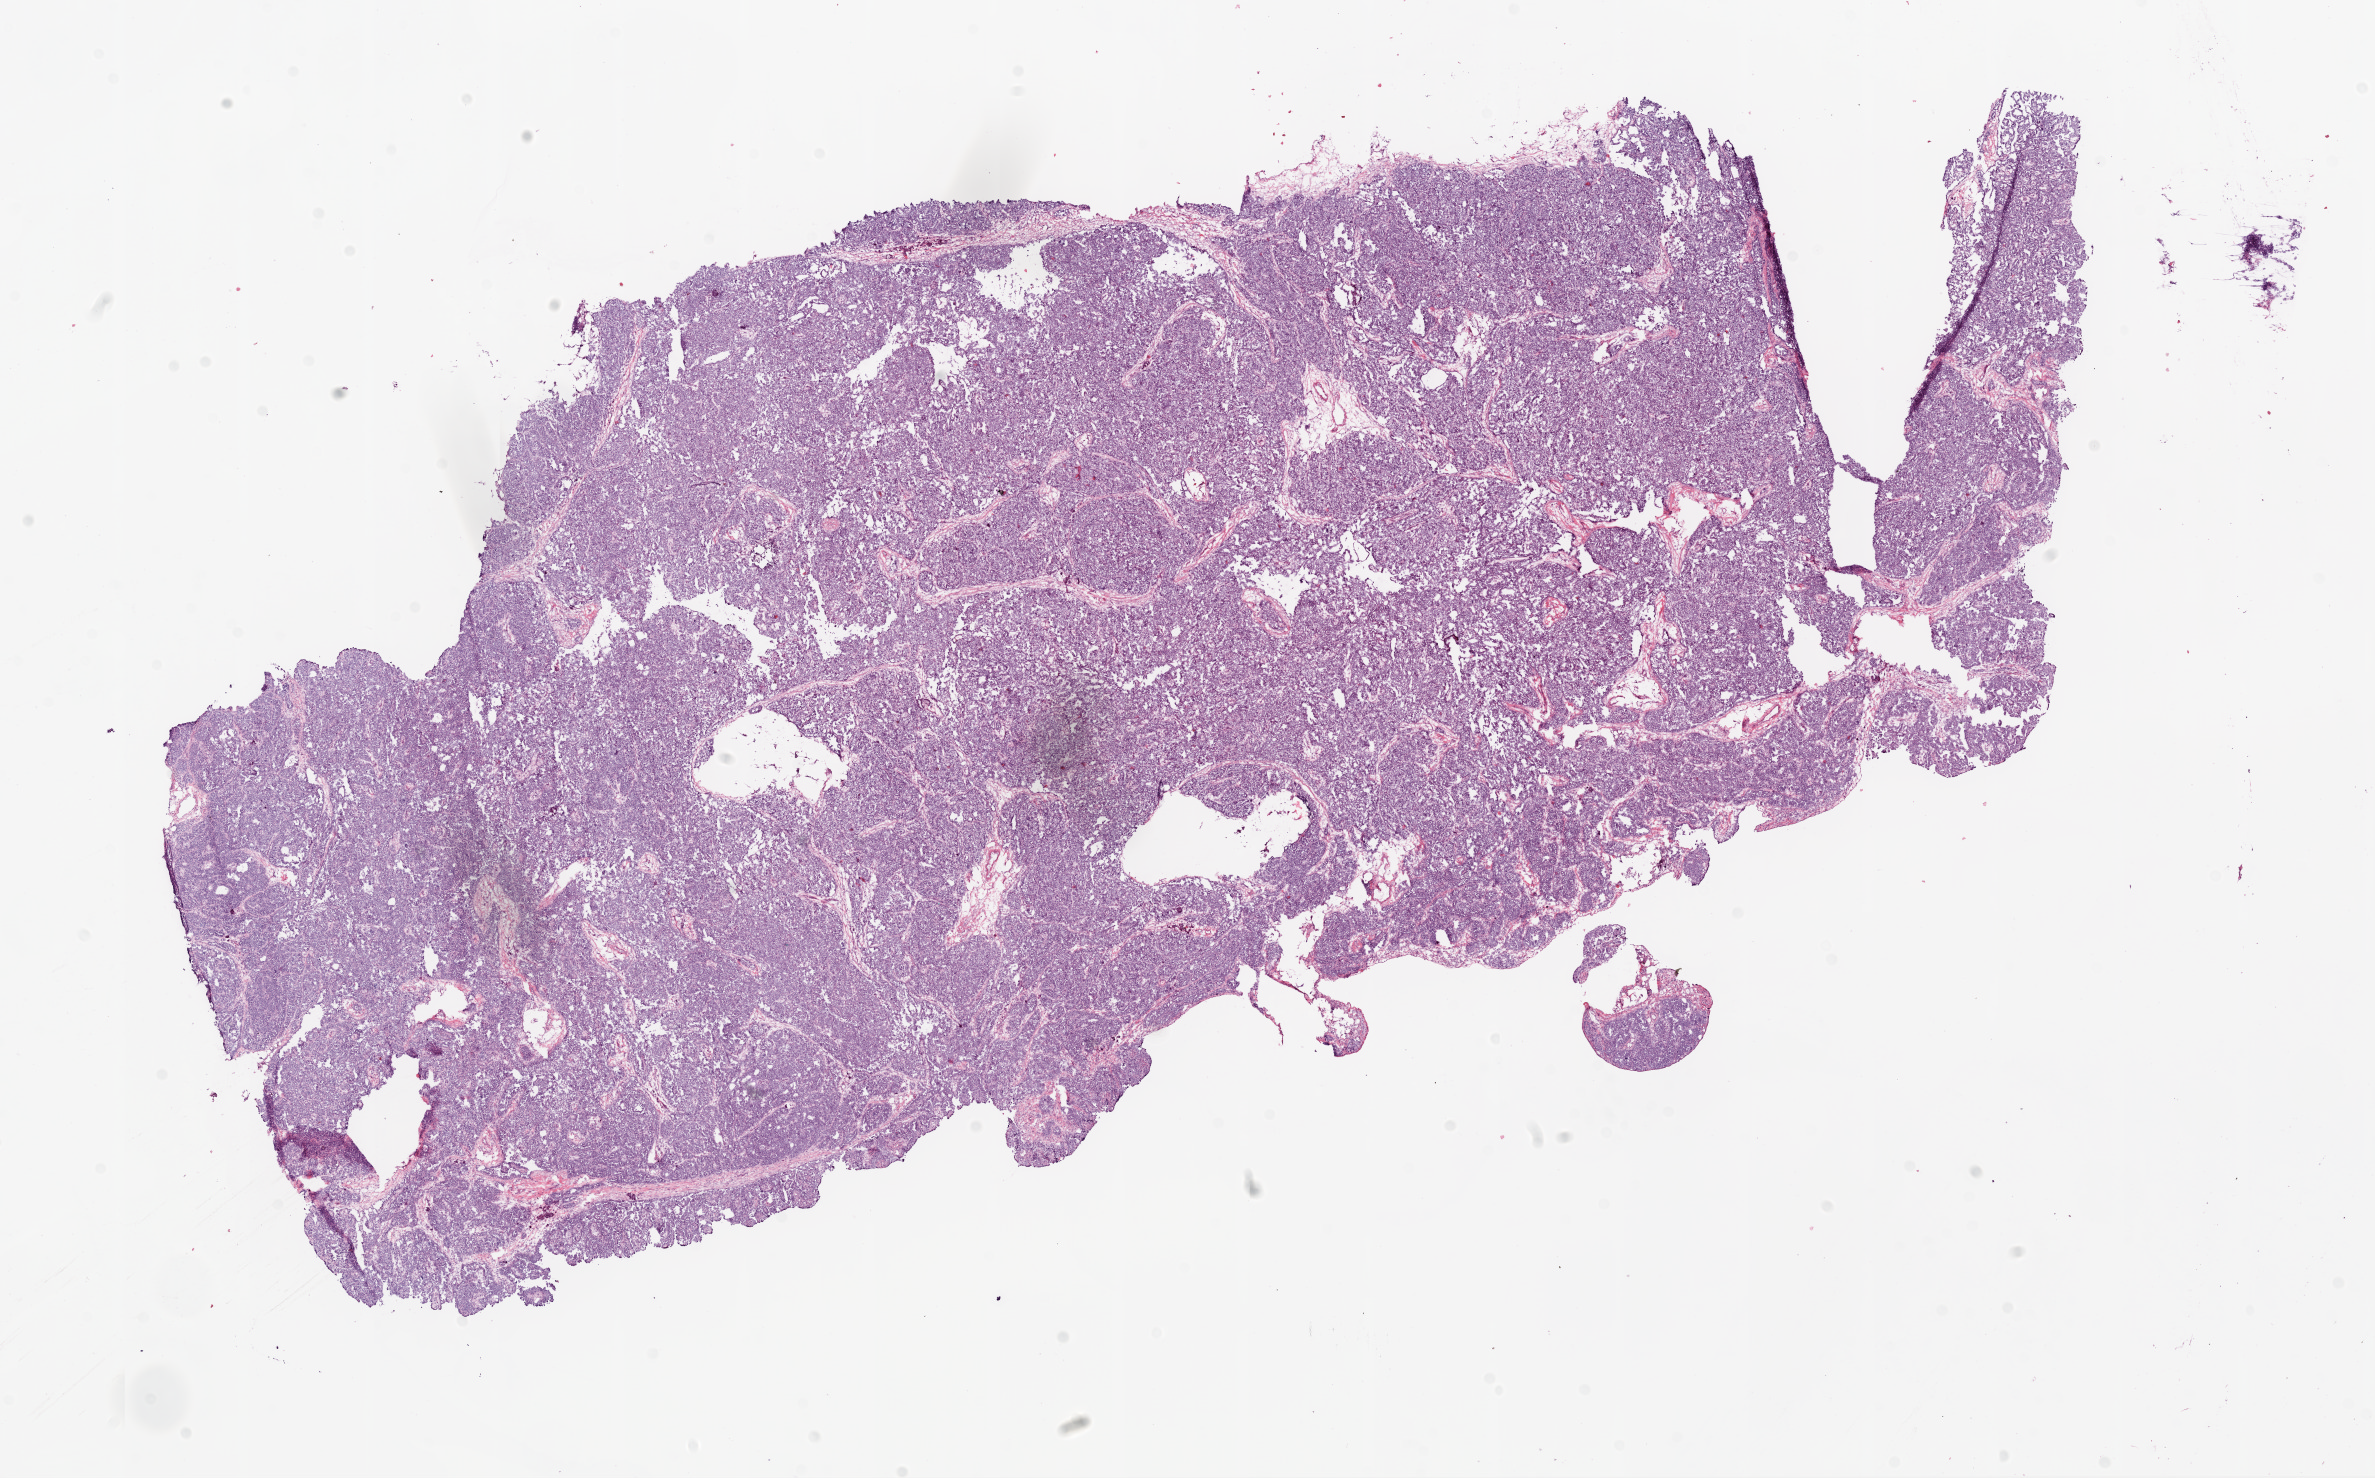
Whole-slide histology image, H&E-stained — whole scanned area (about 19.1 x 11.9 mm) shown as a low-resolution overview. Frozen section from the bottom of the tissue portion. Ovary, primary tumour sample. Female, age 80 years at initial diagnosis. Composition of this section per pathologist review: tumour cells 95%, tumour nuclei 95%, normal cells 0%, stromal cells 5%, necrosis 0%.
Histologic diagnosis: Serous cystadenocarcinoma, NOS.